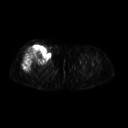
FDG PET of an extremity soft-tissue mass (from a PET/CT study), one axial slice; position 250 of 311 along the scan axis; 3.27 mm slice thickness; 128 × 128 image matrix, field of view 500 × 500 mm. Patient: female, 57 years. From the clinical record (not read from this slice): histological type: pleiomorphic undifferentiated sarcoma; grade: high; site of the primary tumour: right quadricep.
Structures marked on this image (expert contour drawn on MRI and transferred to this co-registered scan by the dataset authors):
- tumour plus oedema (research contour): box from (x=23, y=46) to (x=50, y=72) px
- tumour (research contour): (x=23, y=46)–(x=50, y=72)